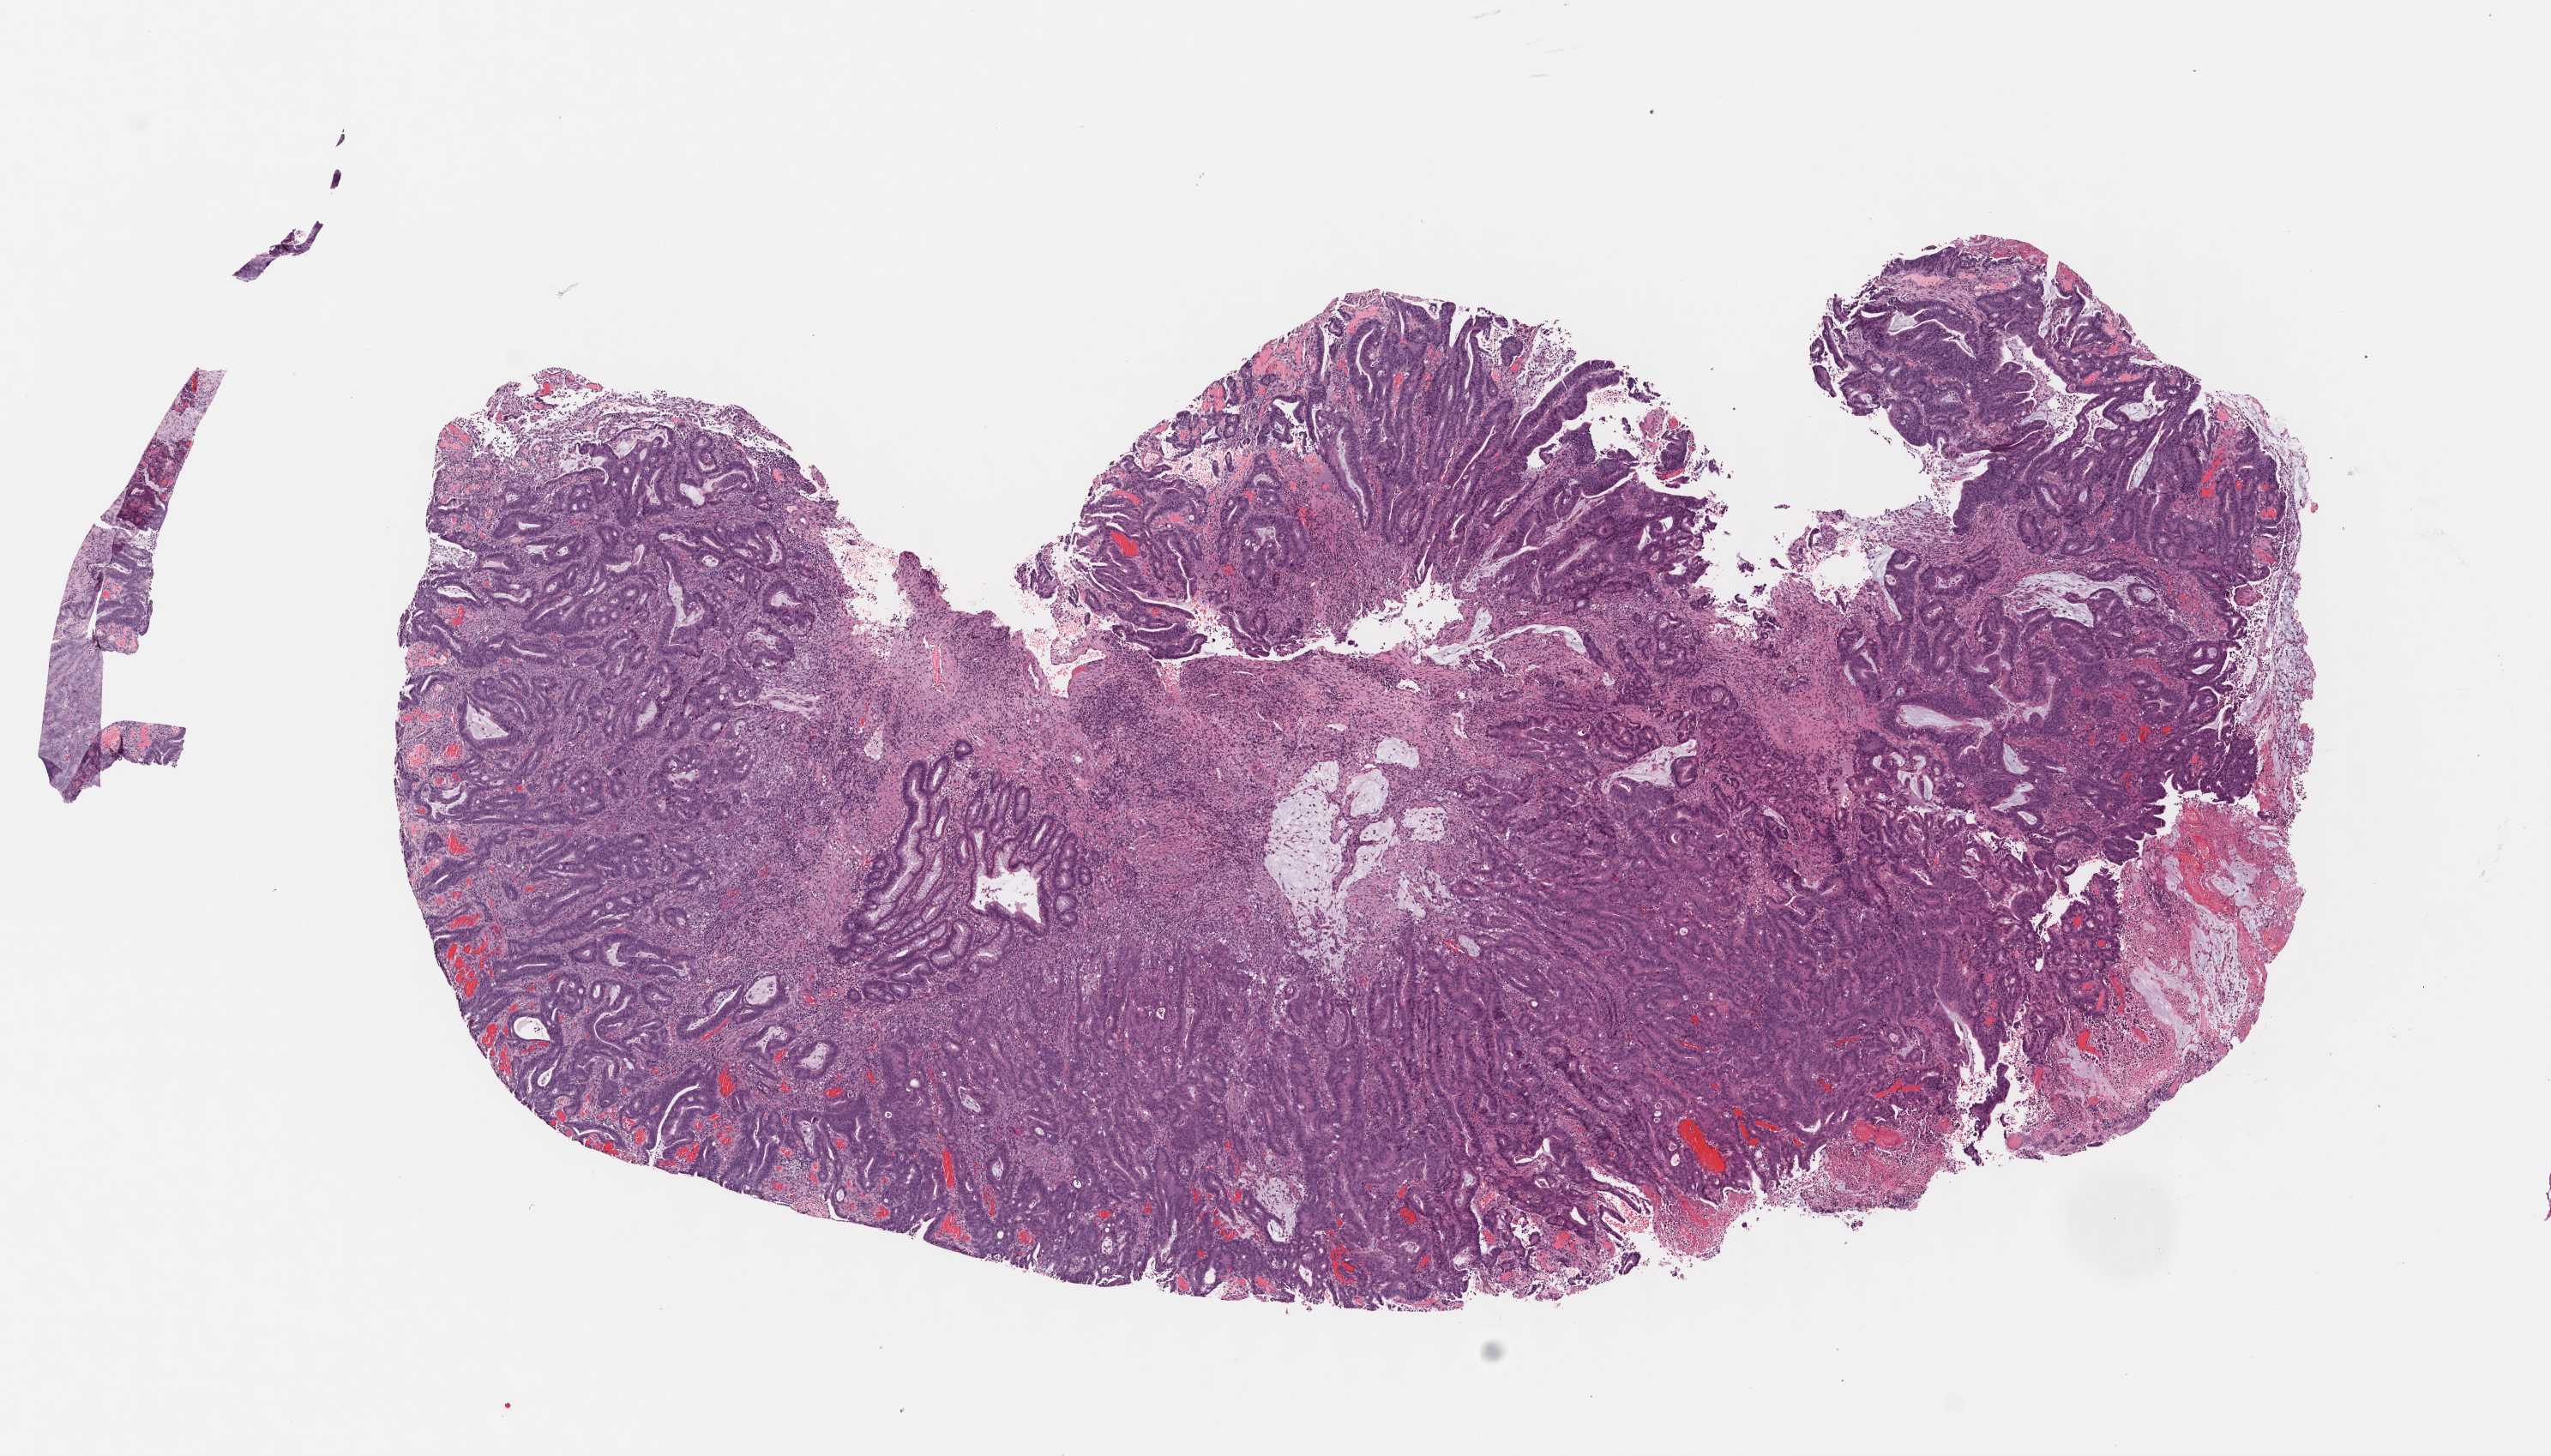
Digitized H&E tissue section (whole slide), a low-resolution overview of the entire scanned area, about 11.7 x 6.7 mm (from a 40x scan). Frozen section. Colon, primary tumour sample. Female patient; age at initial diagnosis 71 years. Pathologist review of this section (percent, as recorded): tumour cells 40%, tumour nuclei 60%, normal cells 10%, stromal cells 35%, necrosis 15%. Inflammatory infiltration, as recorded: lymphocyte infiltration 18%, monocyte infiltration 3%, neutrophil infiltration 3%.
Diagnosis: Mucinous adenocarcinoma. Lymph nodes positive (case pathology): 0 of 24 examined. AJCC pathologic stage: IIB.